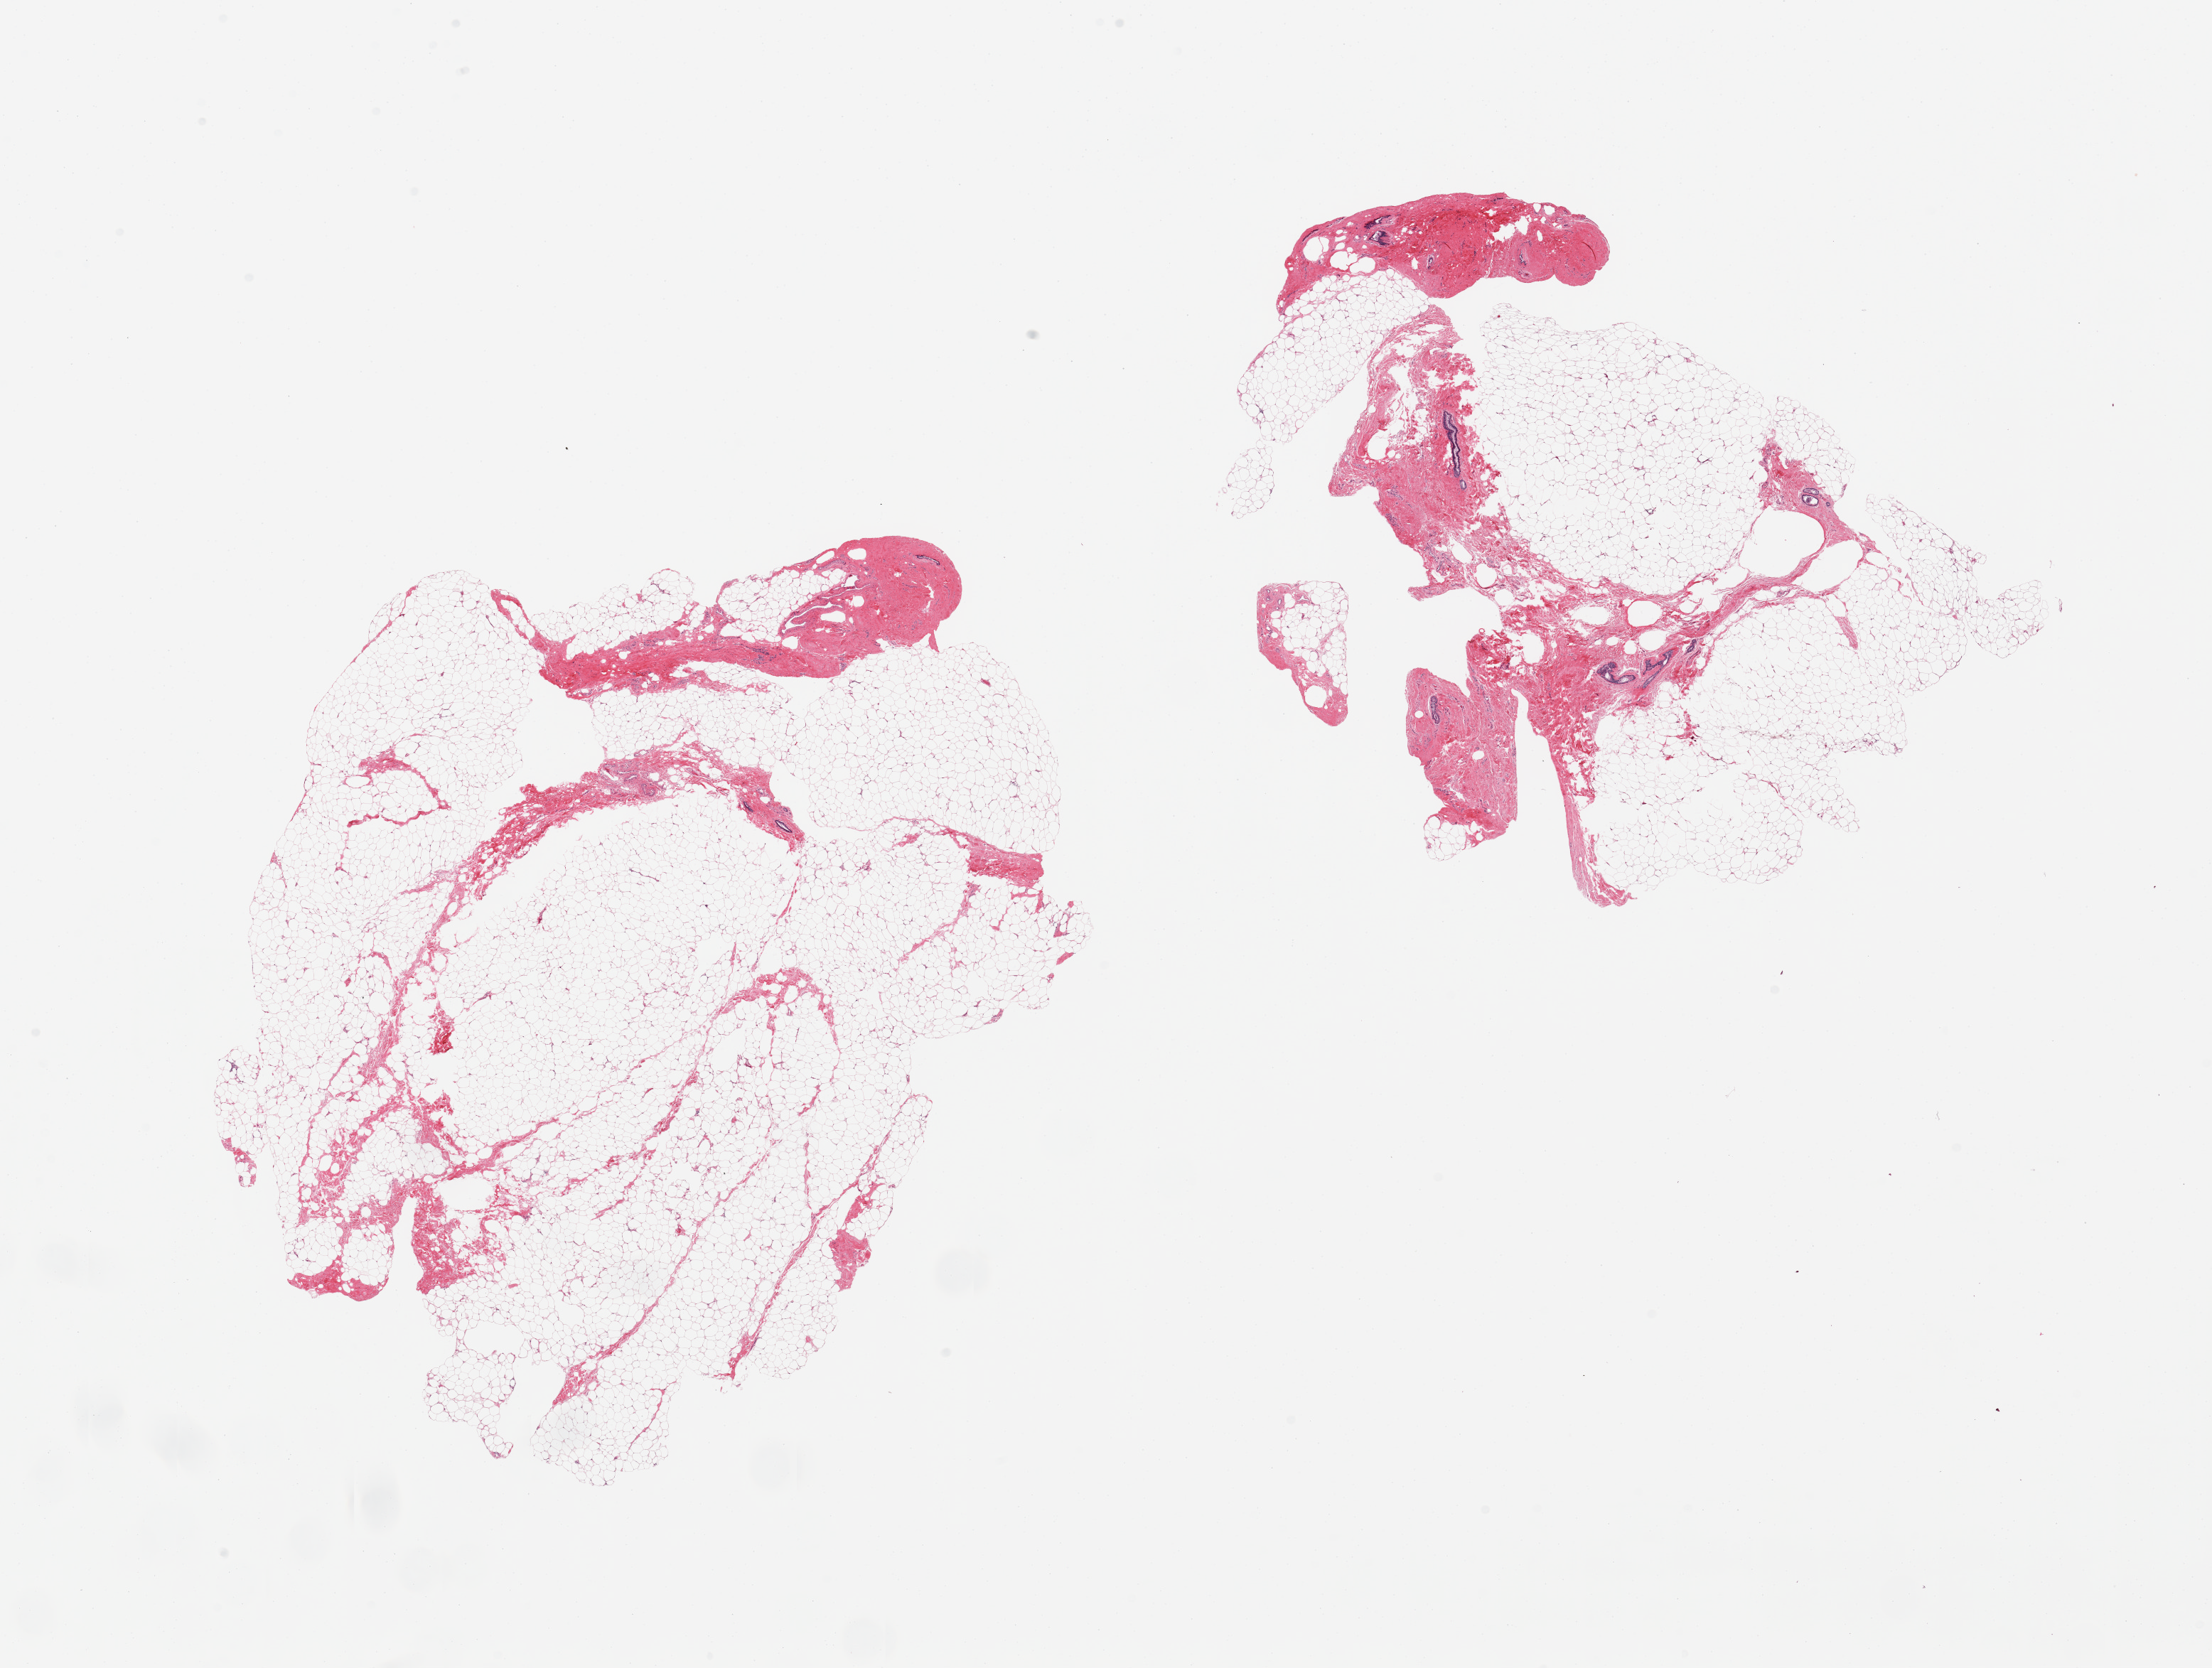
Whole-slide image, hematoxylin and eosin (H&E) stain, low-resolution overview of the scanned area, about 24.6 x 18.6 mm, PAXgene-fixed paraffin-embedded (PFPE) section, target tissue: breast, donor tissue sample. Donor sex: male.
Pathologist's review note for this sample: 2 pieces; predominantly fat with 10-20% fibrous stroma and few ducts.